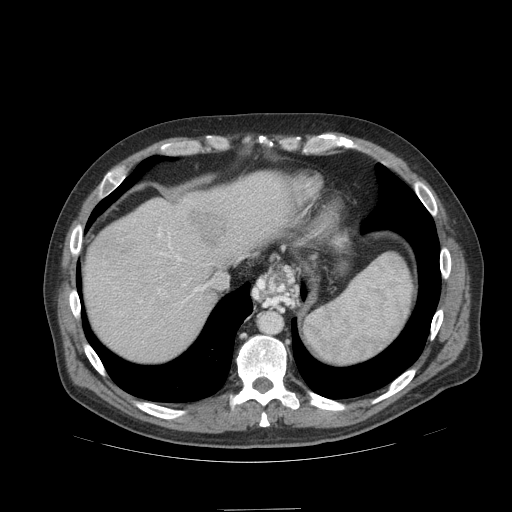
Contrast-enhanced abdominal CT (liver protocol), one axial slice. Slice 85 of 99 in the series (ordered by position). Soft-tissue window (W 400 / L 40 HU). 2.5 mm slice thickness. 512 × 512 image matrix. Case-level facts recorded for this patient, not image findings: diagnosis: hepatocellular carcinoma (patient treated with transarterial chemoembolisation; whether this scan precedes or follows treatment is not stated here); TNM stage (as recorded): Stage-I; Child-Pugh class: A; tumour nodularity: uninodular; tumour size: 3.6 cm.
Annotated regions visible in this slice (semi-automatic segmentation, software-assisted and operator-edited):
- liver parenchyma outside the tumour (the mass and vessels are separate outlines, so this box may not span the whole liver): bounding box (x1, y1, x2, y2) in pixels: (84, 172, 304, 360)
- mass: (190, 209, 228, 246)
- liver vessels: (157, 197, 242, 303)